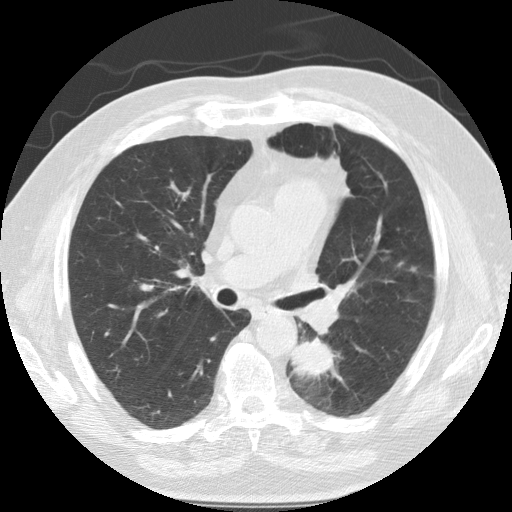
Axial slice from a low-dose chest CT screening exam, baseline screening round, lung window (W 1500 / L -600 HU), 2.5 mm slice thickness, 120 kVp, slice 55 of 124 in the series, 512 × 512 image matrix. Male, age 68 years at enrolment. Former smoker at enrolment.
Expert reader's lesion annotation, bounding box [x1, y1, x2, y2] px = [280, 318, 352, 397]. The screening reader recorded 3 non-calcified nodules or masses ≥4 mm on this exam (left lower lobe, lingula, right lower lobe); which of them this box marks is not recorded. Official screen result: positive, change unspecified: nodule(s) >= 4 mm or enlarging nodule(s), mass(es), or other non-specific abnormalities suspicious for lung cancer. Later outcome: lung cancer diagnosed 35 days after this screen — squamous cell carcinoma, NOS, left lower lobe, poorly differentiated (G3), stage IIB (AJCC 6th edition), 40 mm at pathology.